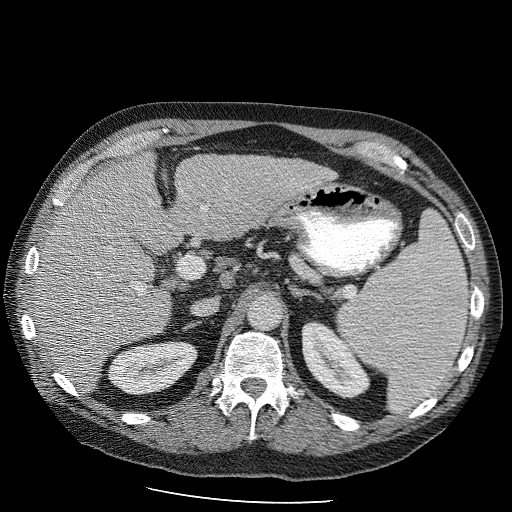
Contrast-enhanced abdominal CT (liver protocol), one axial slice; reconstruction kernel STANDARD; 120 kVp; soft-tissue window (W 400 / L 40 HU); 512 × 512 image matrix, field of view 400 × 400 mm. From the clinical record (not read from this slice): diagnosis: hepatocellular carcinoma (patient treated with transarterial chemoembolisation; whether this scan precedes or follows treatment is not stated here); TNM stage (as recorded): Stage-II; Child-Pugh class: B; tumour differentiation: moderately differentiated; tumour nodularity: uninodular.
Structures marked on this image (semi-automatic segmentation, software-assisted and operator-edited):
- liver parenchyma outside the tumour (the mass and vessels are separate outlines, so this box may not span the whole liver): bounding box [x1, y1, x2, y2] px = [32, 150, 340, 394]
- liver vessels: [141, 202, 210, 290]